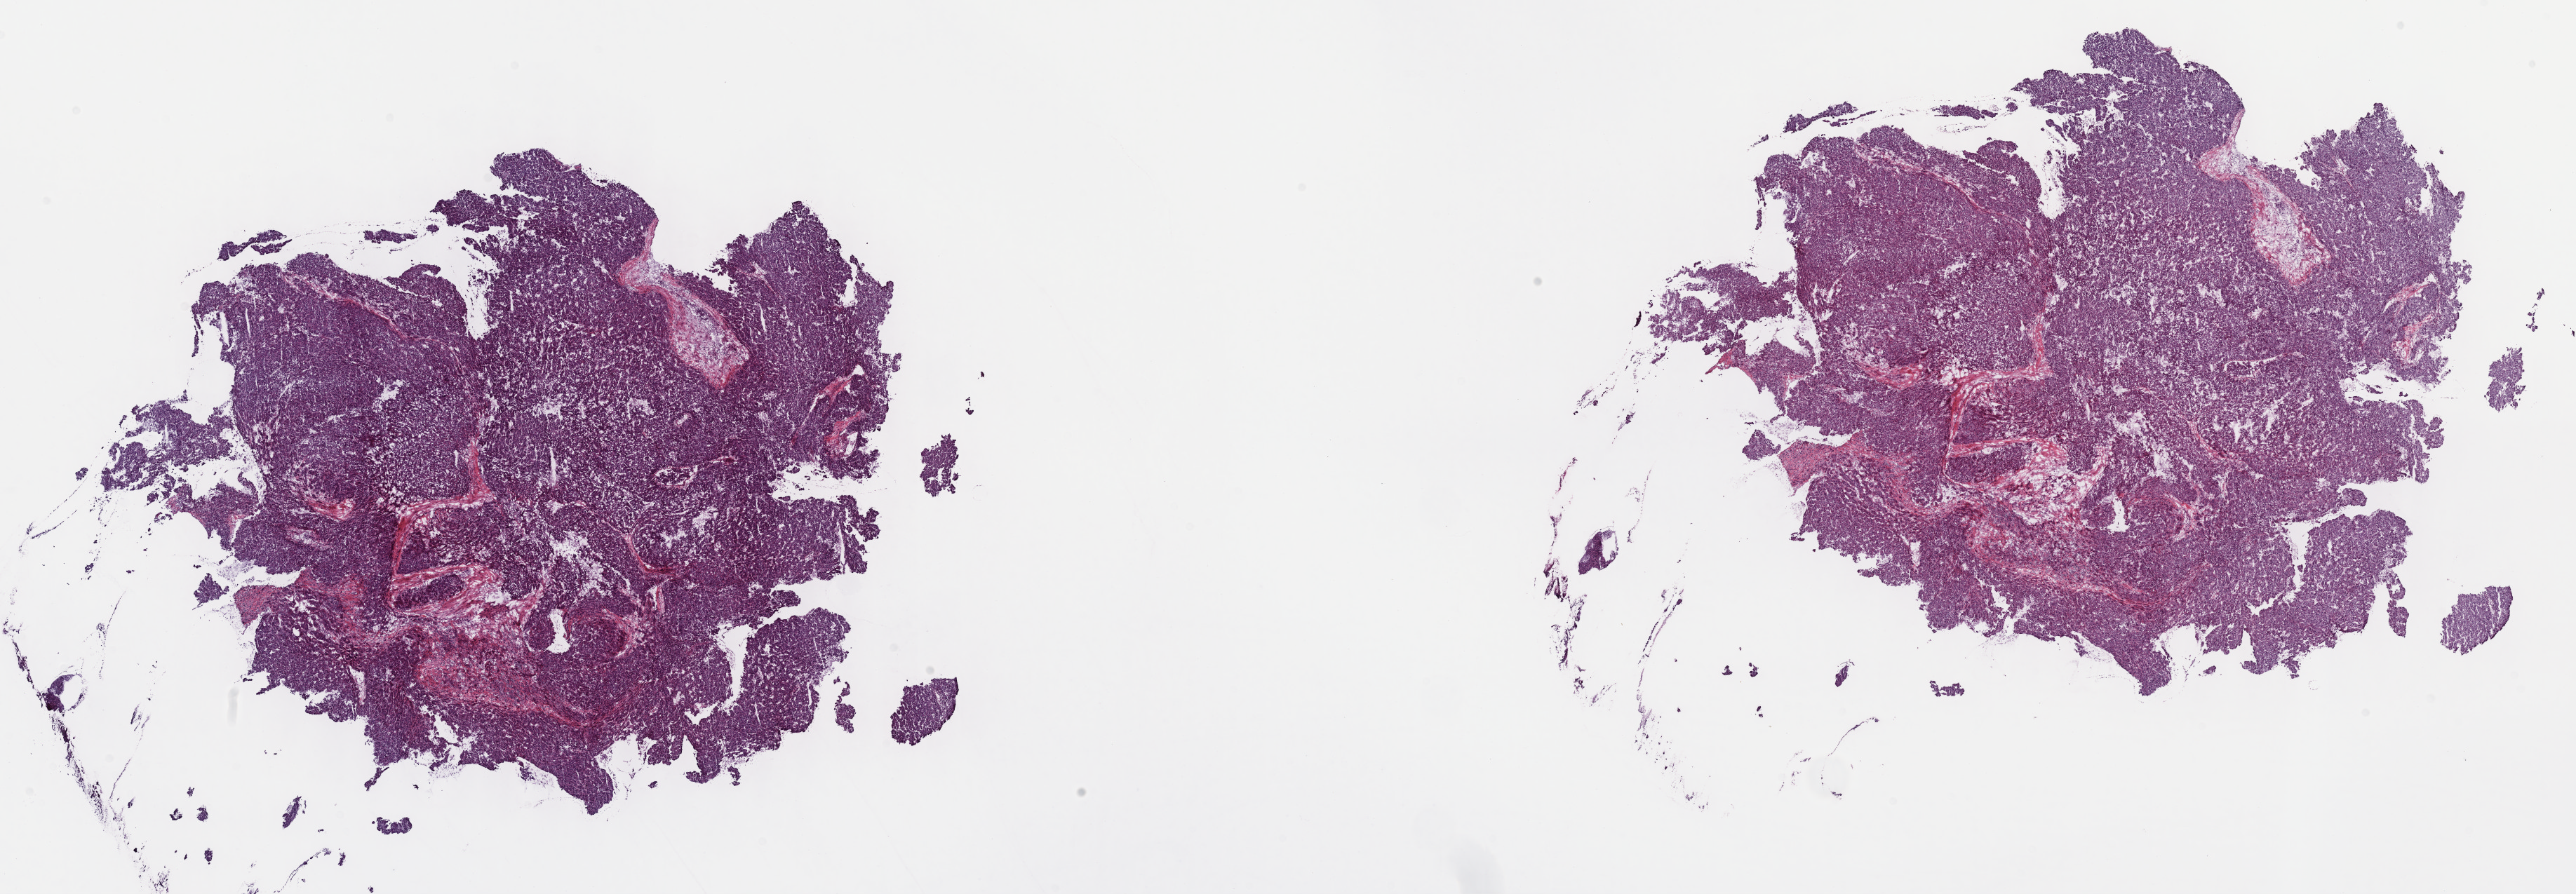
H&E whole-slide image — low-resolution overview of the scanned area, about 29.7 x 10.3 mm, frozen section from the top of the tissue portion, sample: primary tumour, liver. Male patient; age at initial diagnosis 38 years. Histologic grade: G2 (moderately differentiated). Pathologist review of this section (percent, as recorded): tumour cells 75%, tumour nuclei 75%, normal cells 0%, stromal cells 25%, necrosis 0%. Inflammatory infiltration, as recorded: lymphocyte infiltration 5%, monocyte infiltration 1%, neutrophil infiltration 4%.
* histologic diagnosis: Hepatocellular carcinoma, NOS
* AJCC pathologic stage: II (6th edition)